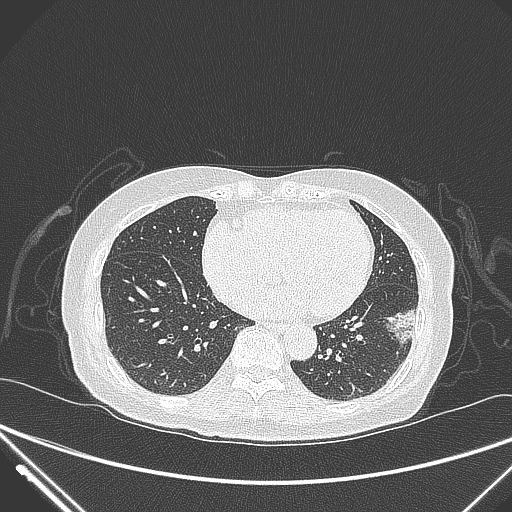
Chest CT, one axial slice. Slice 111 of 310 in the series (ordered by position). Lung window (W 1500 / L -600 HU). 1 mm slice thickness. 512 × 512 image matrix. Patient: female, 82 years. From the clinical record (not read from this slice): clinical TNM (as recorded): T1c N0 M0; histopathological grade: G2.
Outlined on this slice (bounding box drawn by a radiologist):
- lung tumour (recorded histology: adenocarcinoma): box from (x=378, y=303) to (x=424, y=351) px